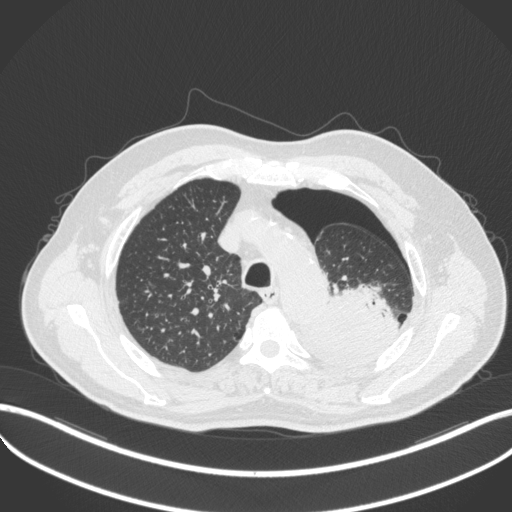
Chest CT, one axial slice; position 389 of 466 along the scan axis; reconstruction kernel B31f; 120 kVp; lung window (W 1500 / L -600 HU); 512 × 512 image matrix. Male patient, age 76 years. Case-level facts recorded for this patient, not image findings: clinical TNM (as recorded): T3 N0 M1b.
Annotated regions visible in this slice (bounding box drawn by a radiologist):
- lung tumour (recorded histology: adenocarcinoma): bounding box [x1, y1, x2, y2] px = [308, 291, 384, 375]